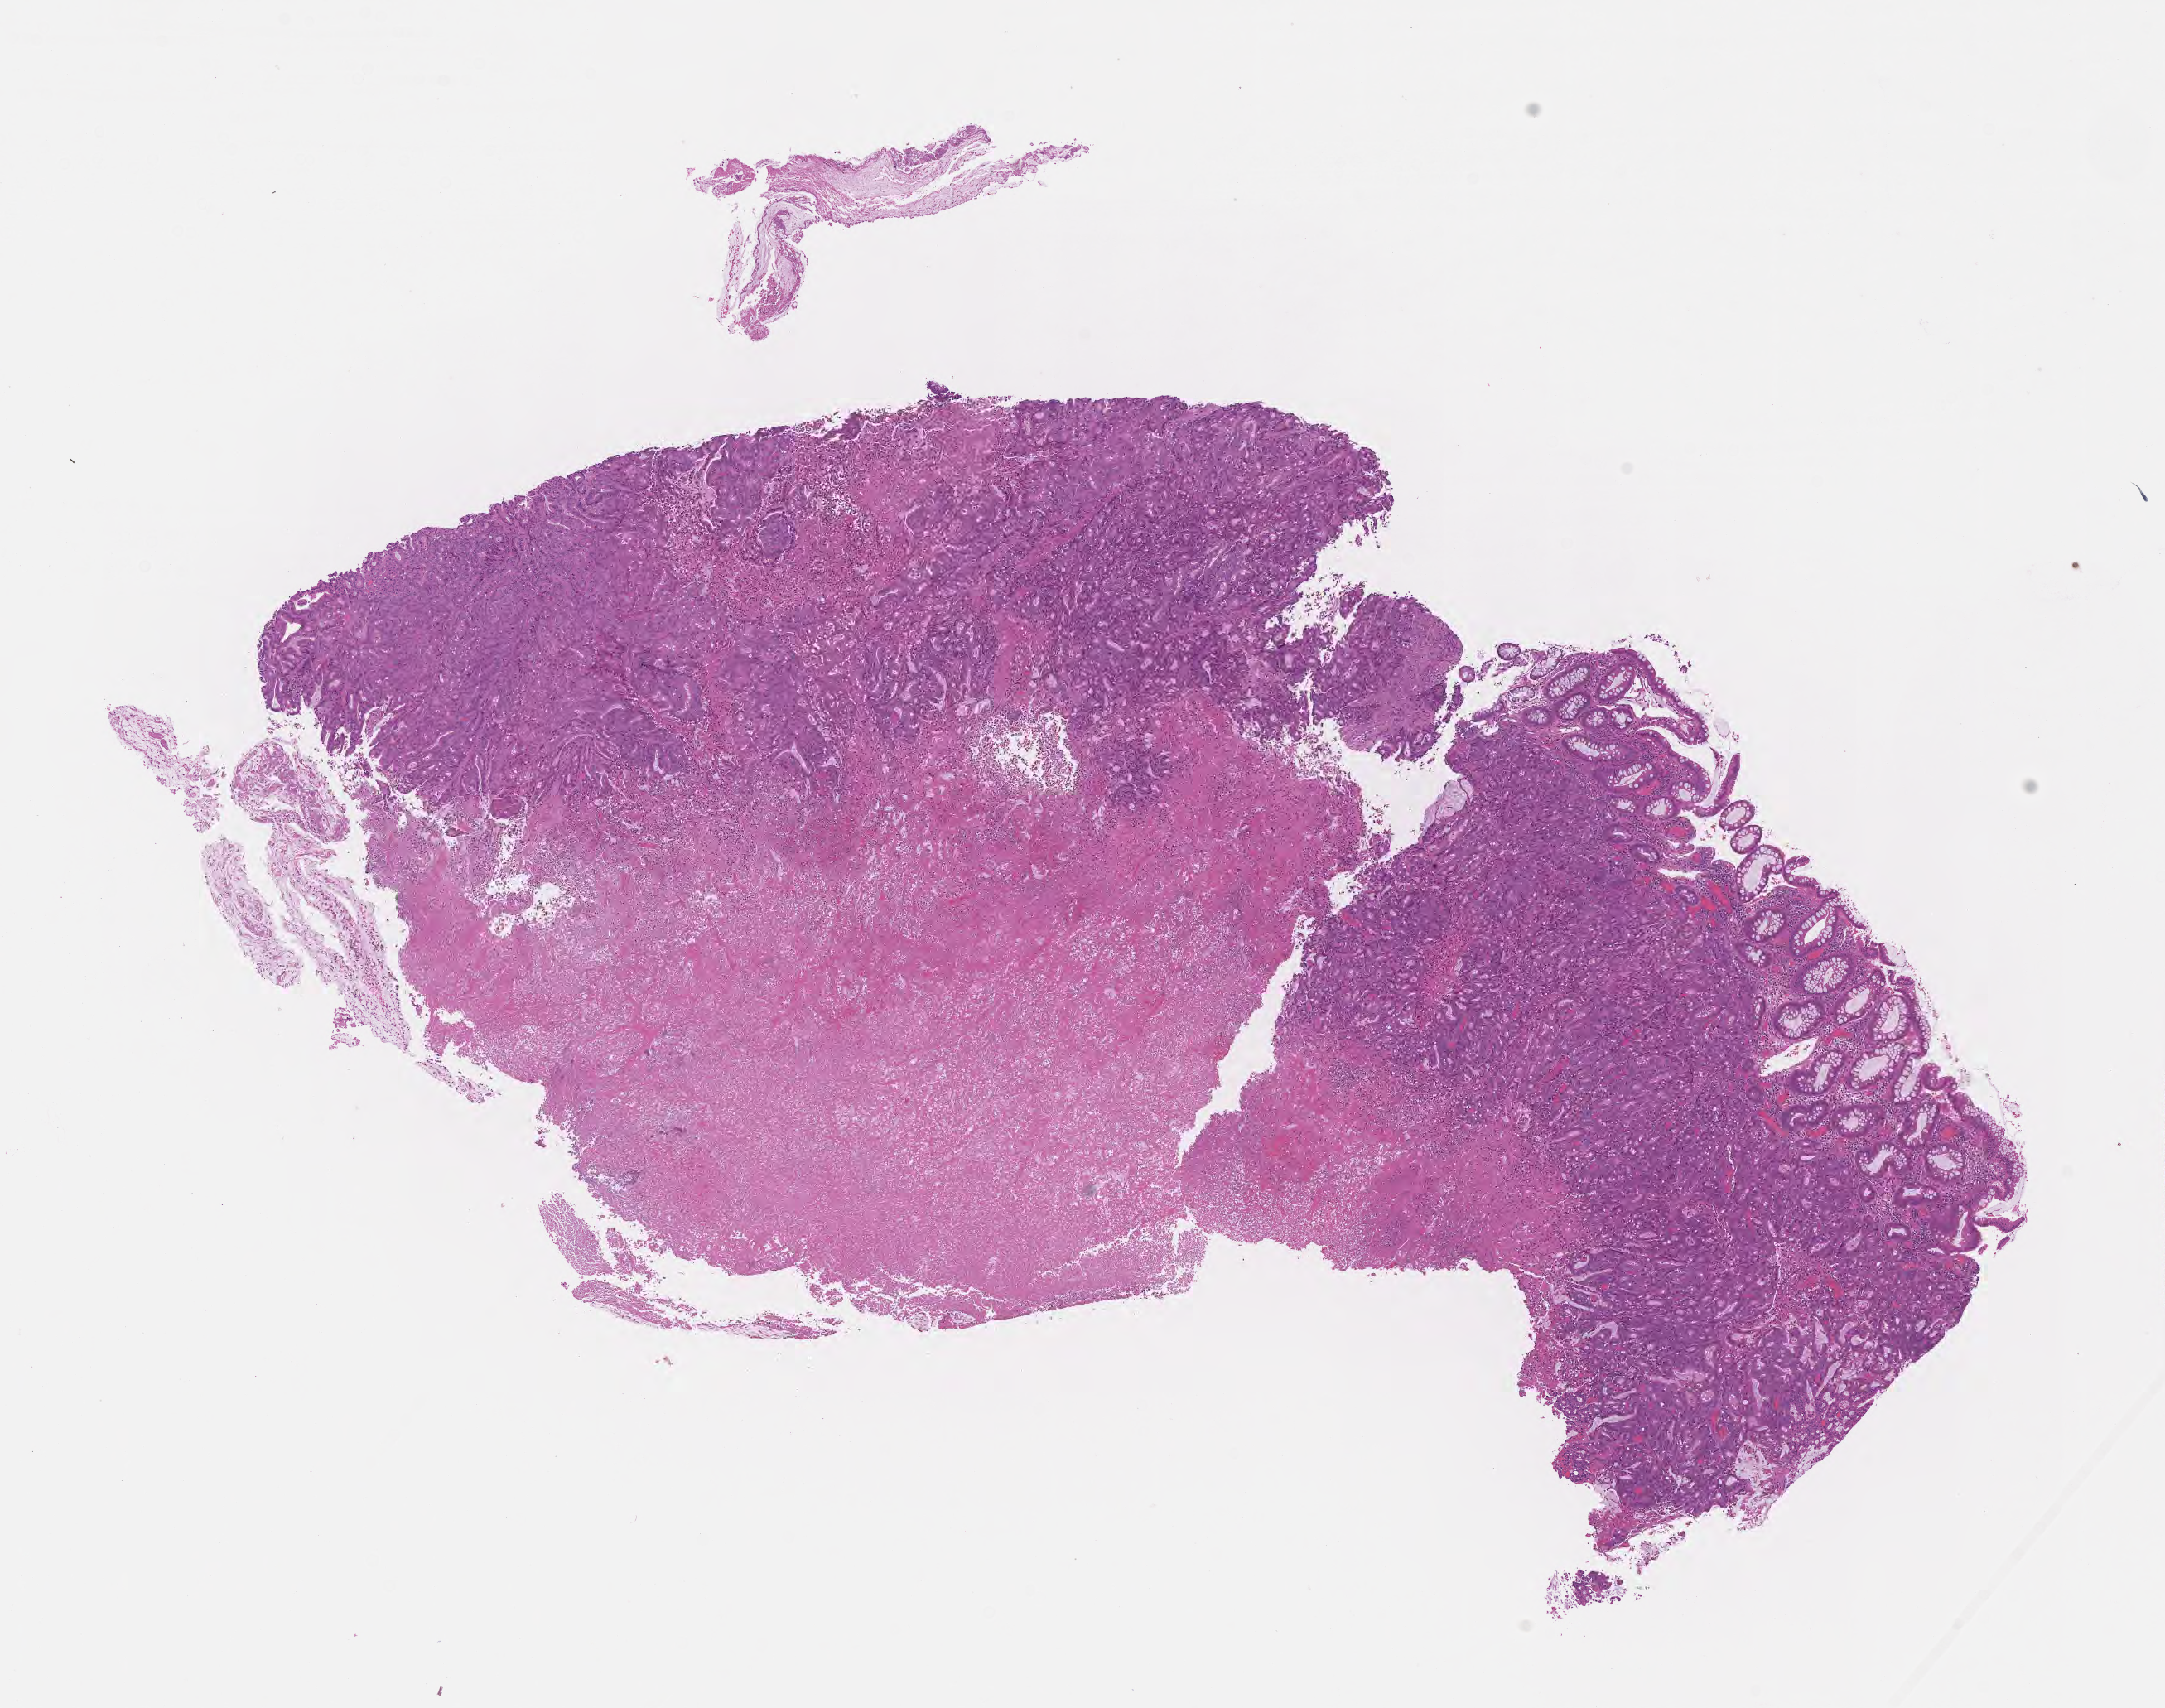
Hematoxylin and eosin (H&E) whole-slide image — shown as a low-resolution overview of the whole scanned area (about 10.6 x 8.3 mm), formalin-fixed paraffin-embedded section, primary tumor, anatomic site: splenic flexure of colon. Male patient; age at initial diagnosis 72 years. Tumor grade: G2 (moderately differentiated). Pathologist review of this section (percent, as recorded): tumor cells 50%, tumor nuclei 50%, stromal cells 10%, necrosis 35%, normal cells 5%. Infiltration values recorded for this section: lymphocyte infiltration 2%, monocyte infiltration 1%, neutrophil infiltration 3%.
• histologic diagnosis: Adenocarcinoma, NOS
• section: bottom of the tissue portion
• AJCC pathologic stage: Stage IIA